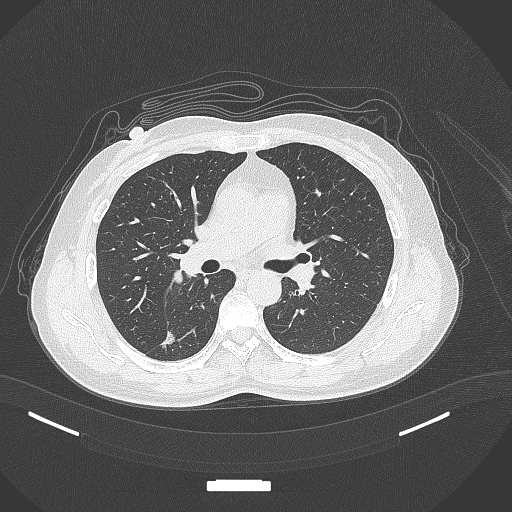
Chest CT, one axial slice. Position 178 of 352 along the scan axis. Reconstruction kernel B70f. 120 kVp. Lung window (W 1500 / L -600 HU). 512 × 512 image matrix, field of view 400 × 400 mm. Patient: female, 55 years. Case-level facts recorded for this patient, not image findings: clinical TNM (as recorded): T1c N1 M0.
Annotated regions visible in this slice (bounding box drawn by a radiologist):
- lung tumour (recorded histology: adenocarcinoma): box from (x=158, y=326) to (x=180, y=350) px